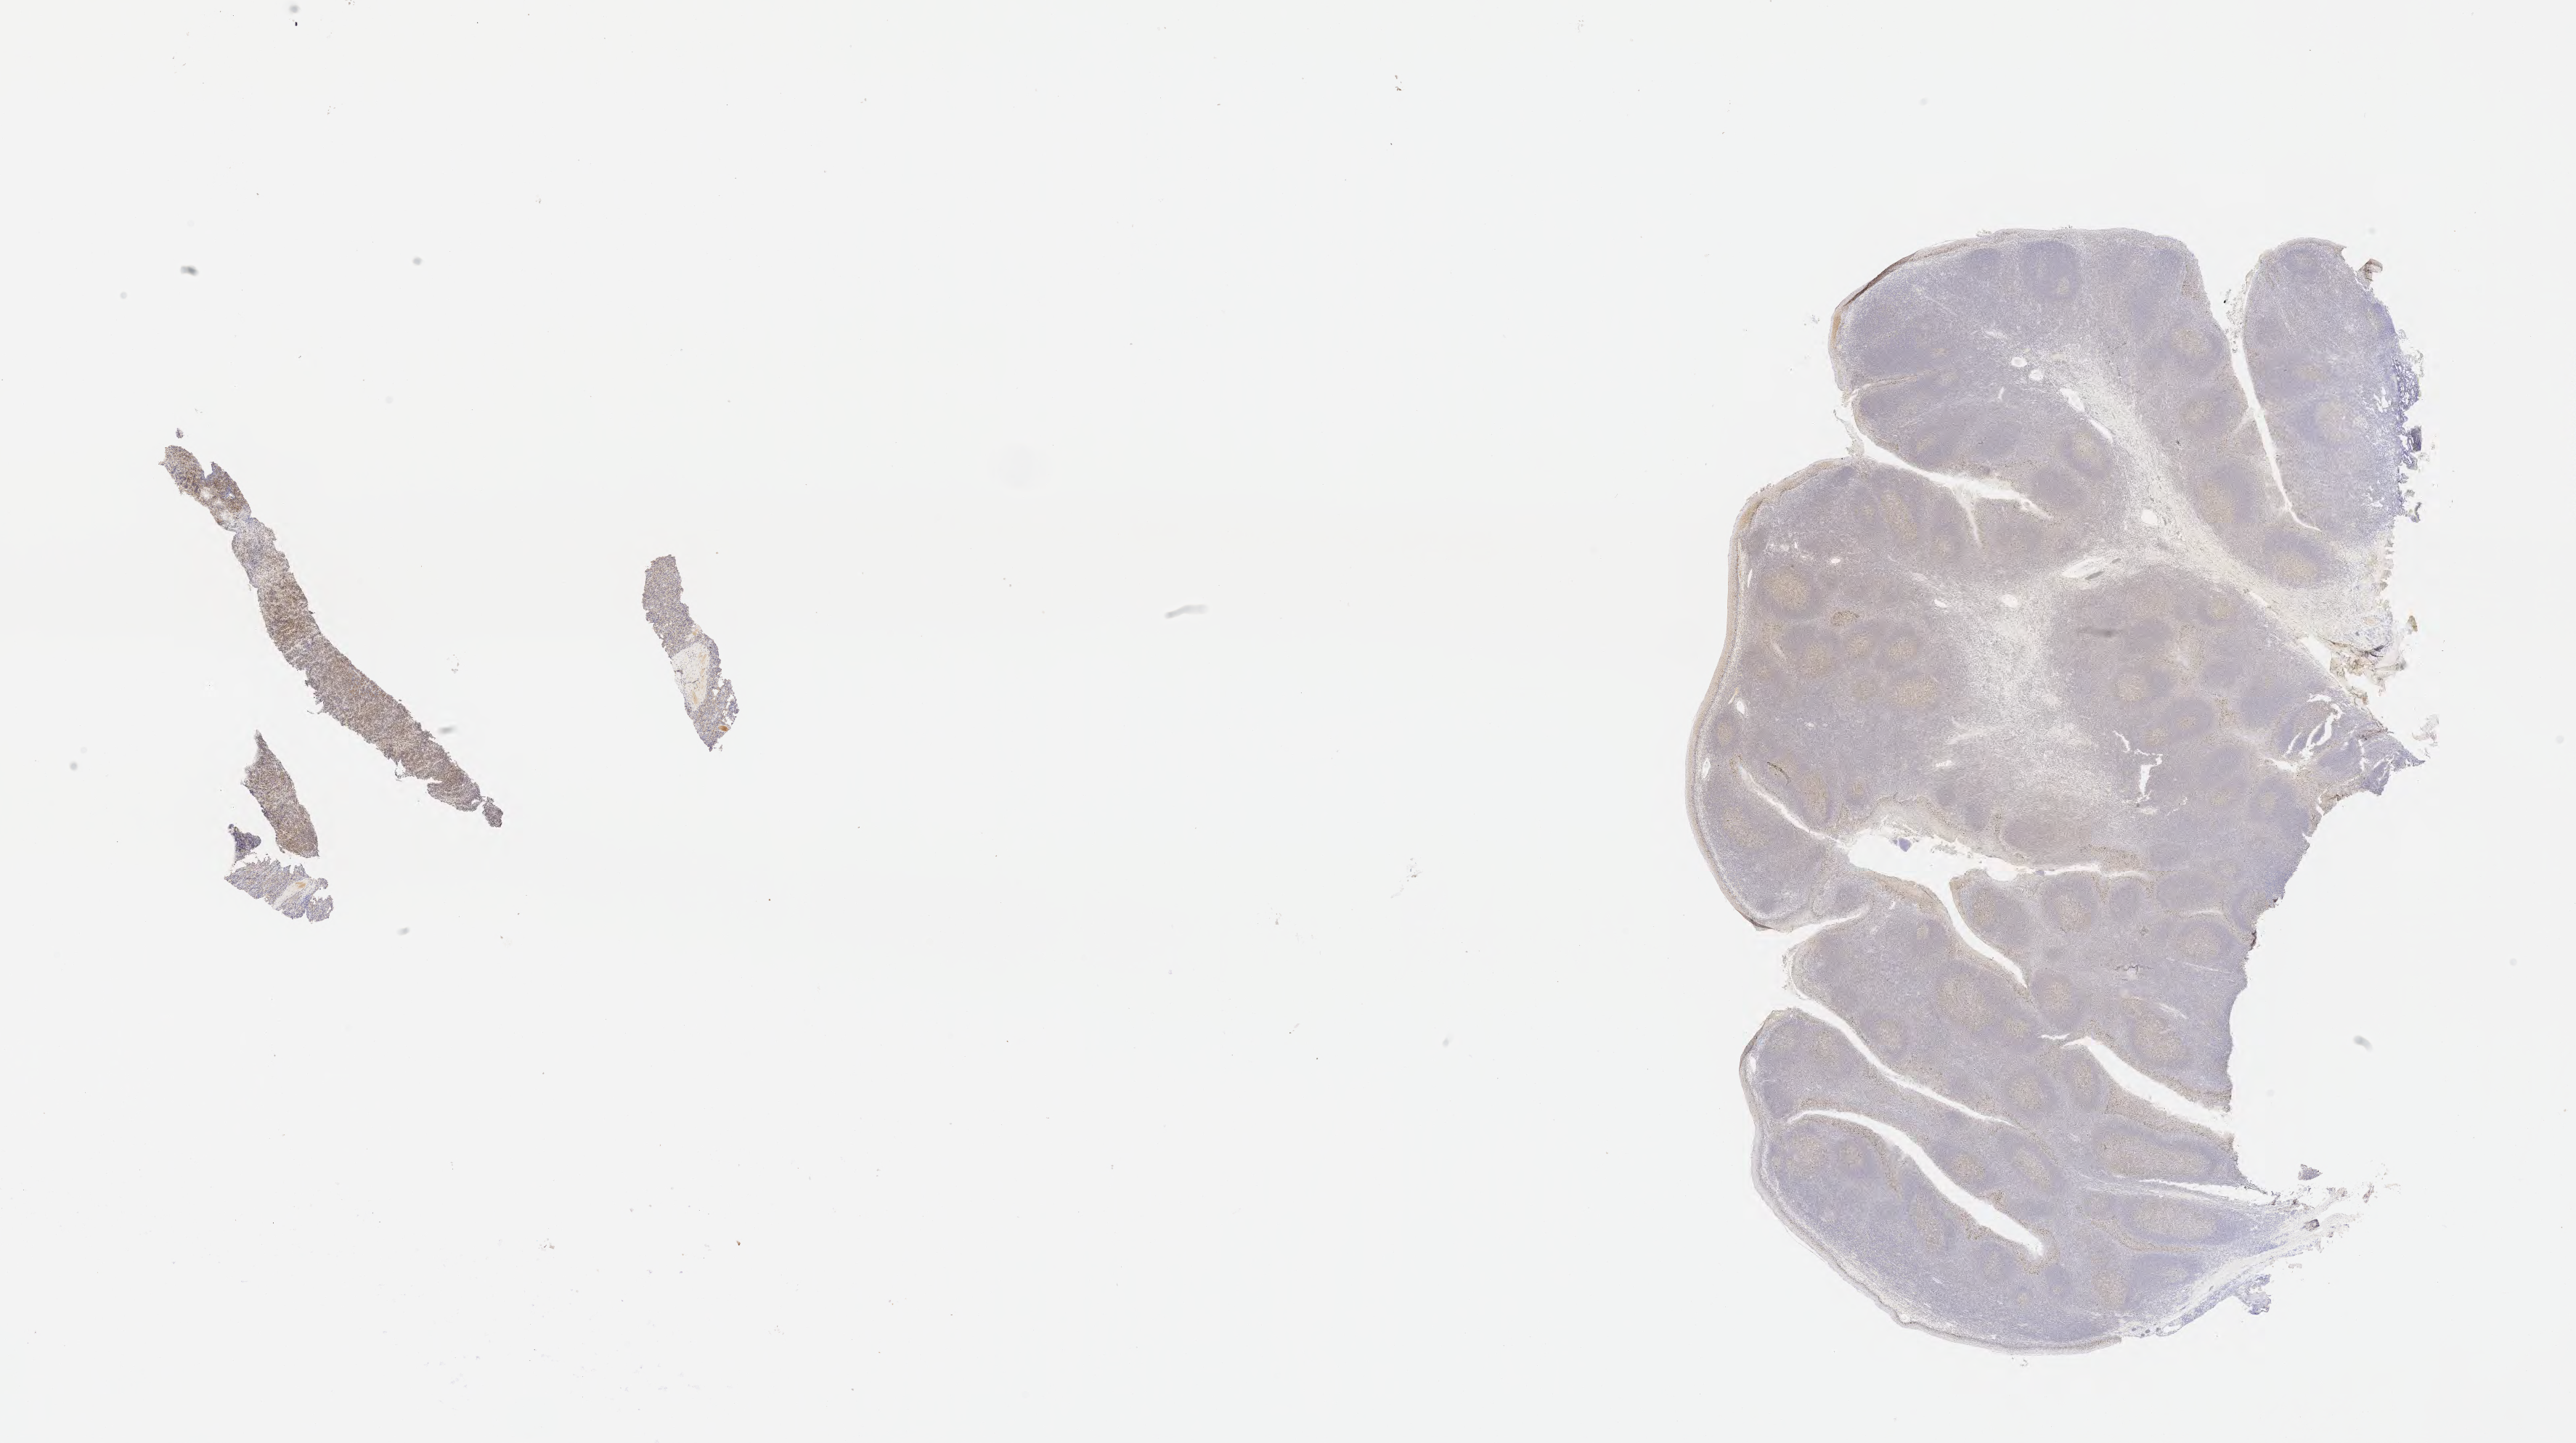
Whole-slide image, immunohistochemical stain for p53 — whole scanned area (about 28.7 x 16.1 mm) shown as a low-resolution overview. Specimen: tumor tissue. Male patient, 13 years old.
Diagnosis: Diffuse large B-cell lymphoma, NOS.